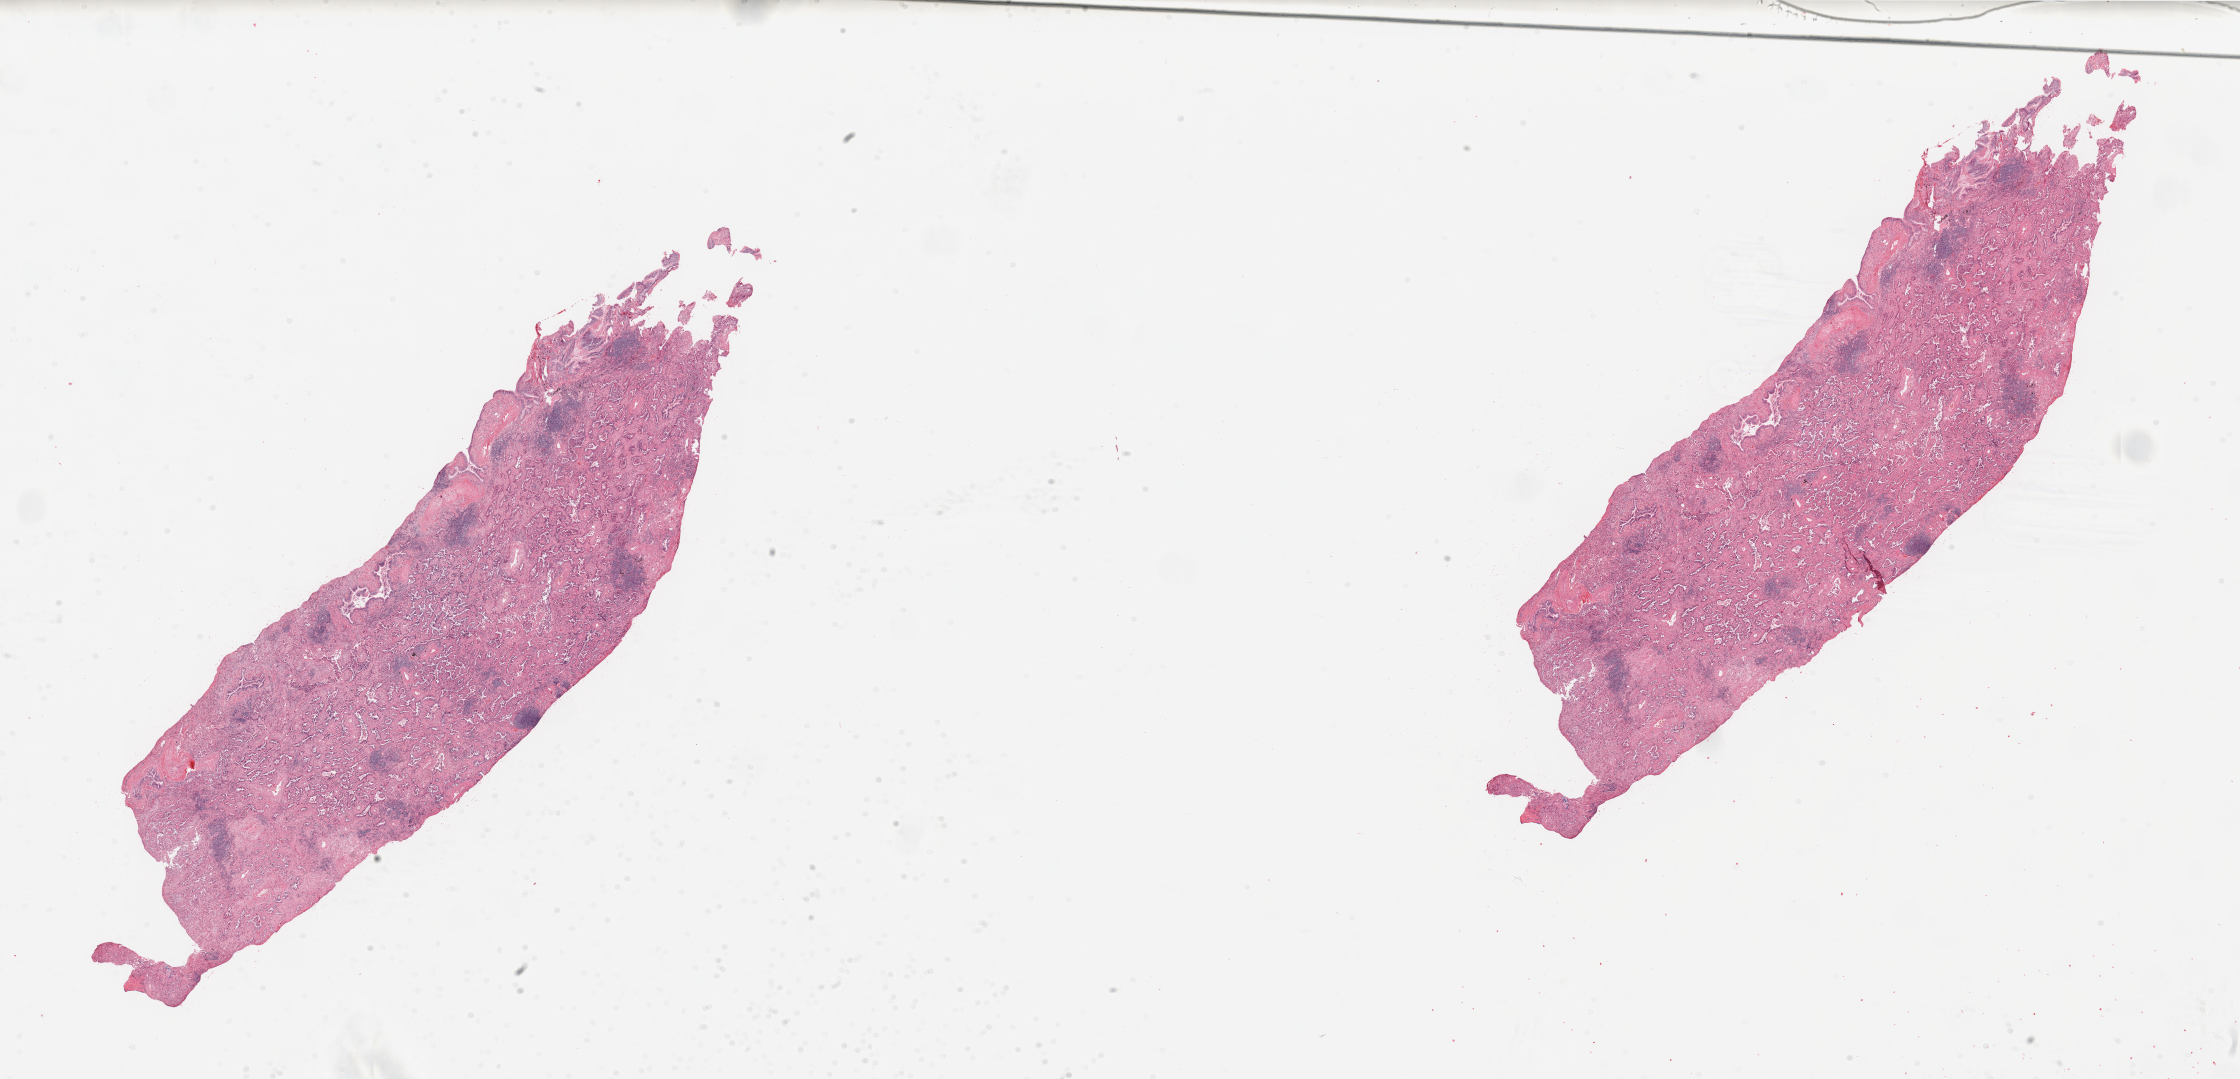
Digitized Hematoxylin and eosin (H&E) stained tissue section (whole slide) — shown as a low-resolution overview of the whole scanned area (about 35.4 x 17.1 mm, acquisition: 20x scan); lung, tumour tissue. Patient: male, age 65 years. Histologic grade: G2 (moderately differentiated).
• AJCC pathologic stage: IA
• primary tumour site (as recorded): left upper lobe
• diagnosis: Adenocarcinoma, NOS